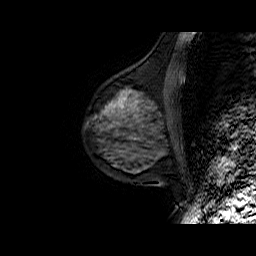
Breast MRI (dynamic contrast-enhanced), one sagittal slice. Position 22 of 50 along the scan axis. Dynamic contrast-enhanced series, time point 2 of 6 at this slice position (early post-contrast). 1.5 T. TE 6.5 ms, TR 32.9 ms. 4 mm slice thickness. 256 × 256 image matrix, field of view 200 × 200 mm. Female patient. From the clinical record (not read from this slice): setting: breast cancer imaged before/during neoadjuvant chemotherapy; receptor status: HR-positive, HER2-negative.
Outlined on this slice (semi-automatically segmented with operator editing):
- analysis volume of interest (the breast-tissue region the enhancement analysis was run in; not a lesion): bounding box <85,75,179,149> (left, top, right, bottom; pixels)
- tumour enhancement mask (voxels above the 100 % enhancement threshold inside the analysis volume of interest): <109,104,123,112>